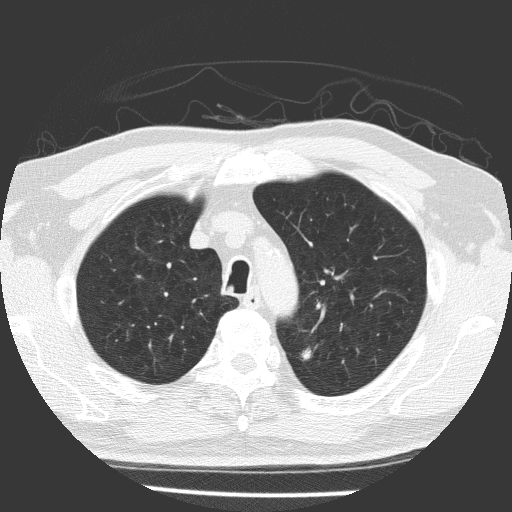
Axial slice from a low-dose chest CT screening exam; first (baseline) screen; lung window (W 1500 / L -600 HU); 2 mm slice thickness; lung (sharp) reconstruction kernel (FC51); slice 38 of 169 in the series. Male, age 64 years at enrolment.
- Expert-annotated lung lesion, bounding box (x1, y1, x2, y2) in pixels: (288, 338, 325, 374).
- Reader record for this screening exam (exam-level; its link to the box is not recorded): non-calcified nodule or mass ≥4 mm, left upper lobe, 9 × 7 mm, spiculated (stellate) margins, soft tissue attenuation.
- Later outcome: lung cancer diagnosed 70 days after this screen — adenocarcinoma, NOS, left upper lobe, poorly differentiated (G3), stage IIA (AJCC 6th edition), 9 mm at pathology.